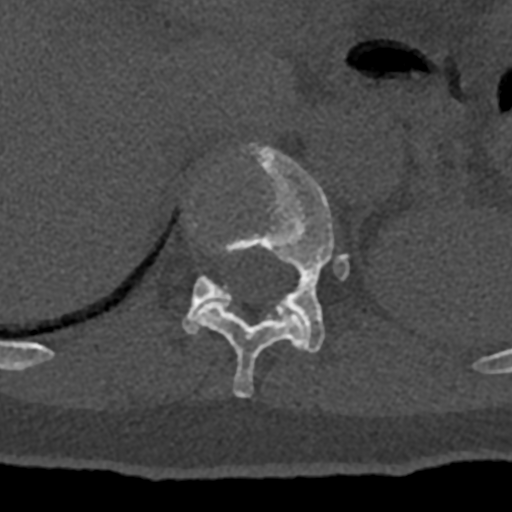
CT including the spine, one axial slice; slice 522 of 797 in the series (ordered by position); reconstruction kernel Br40s/3; 120 kVp; bone window (W 1800 / L 400 HU); 512 × 512 image matrix, field of view 160 × 160 mm. Patient: male, 74 years. From the clinical record (not read from this slice): primary cancer: renal; vertebrae with lytic lesions (as recorded): T10, L1, L2, L3, L4, L5.
Structures marked on this image (semi-automatically segmented with operator editing):
- T11 vertebra: box from (x=193, y=301) to (x=307, y=398) px
- T12 vertebra: (x=182, y=142)–(x=349, y=353)